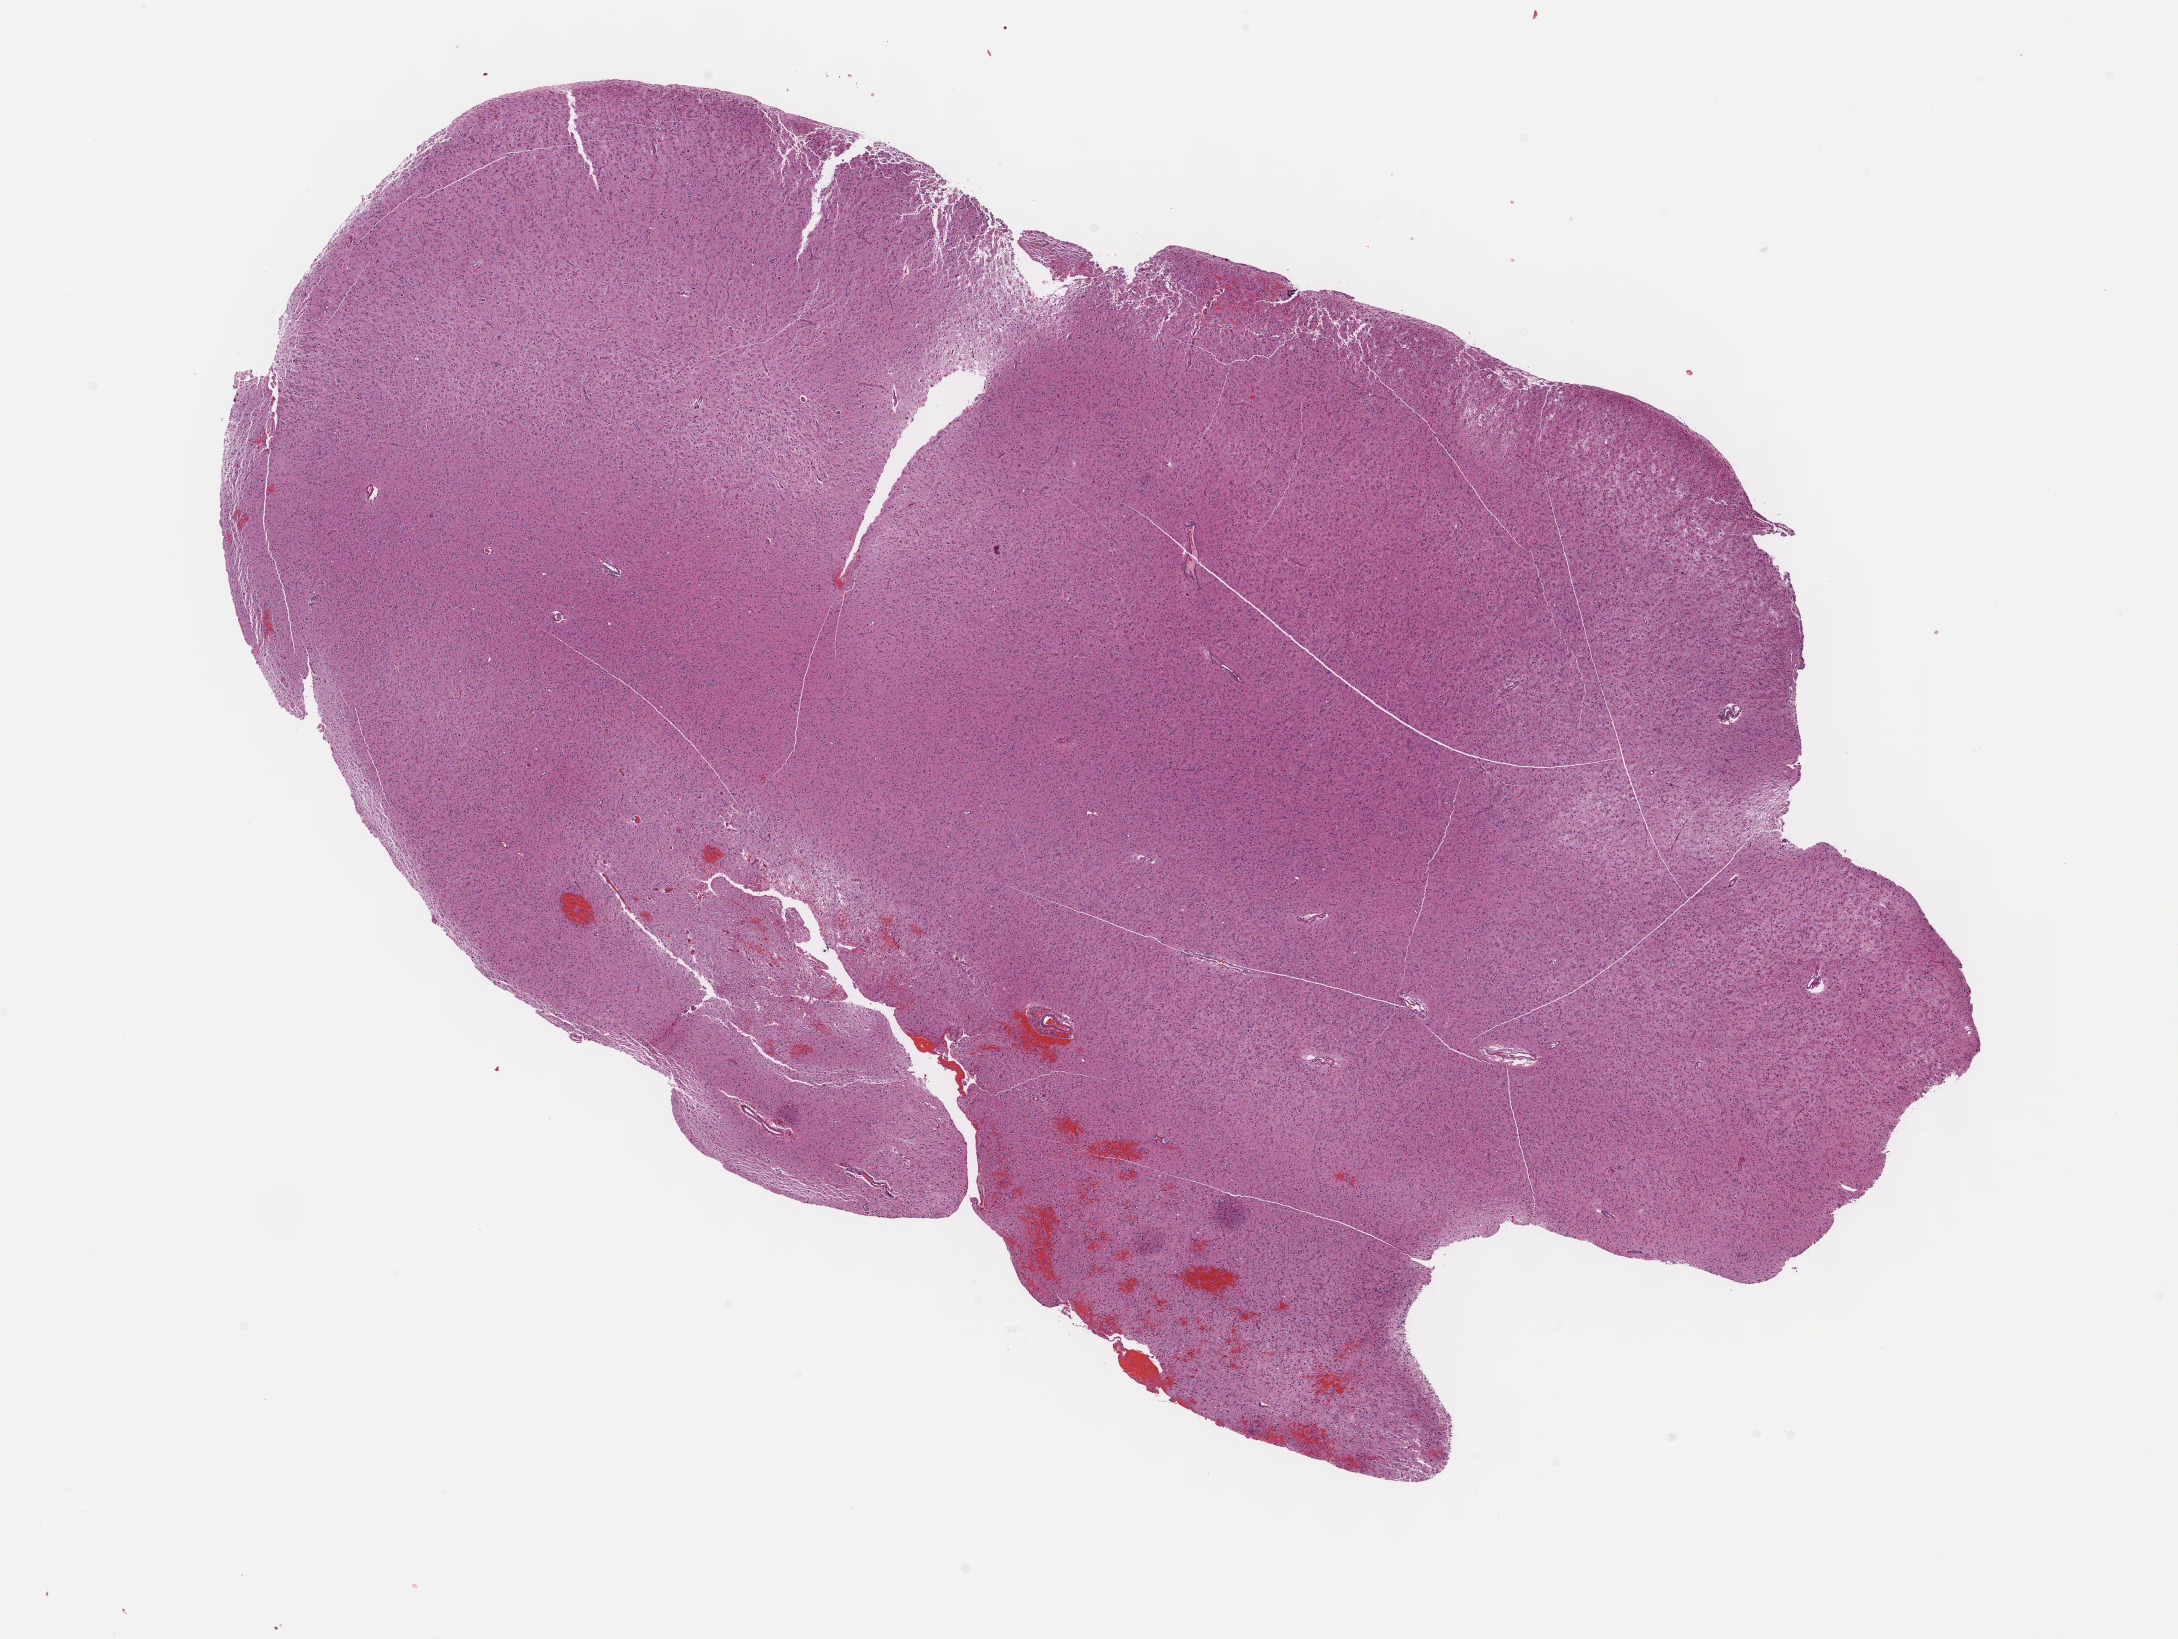
Digitized H&E tissue section (whole slide) — a low-resolution overview of the entire scanned area, about 17.6 x 13.3 mm (slide scanned at 40x). Formalin-fixed paraffin-embedded (FFPE) diagnostic section. Brain, primary tumour sample. Female, age 30 years at initial diagnosis. Histologic grade: G3 (poorly differentiated).
Histologic diagnosis: Astrocytoma, anaplastic.